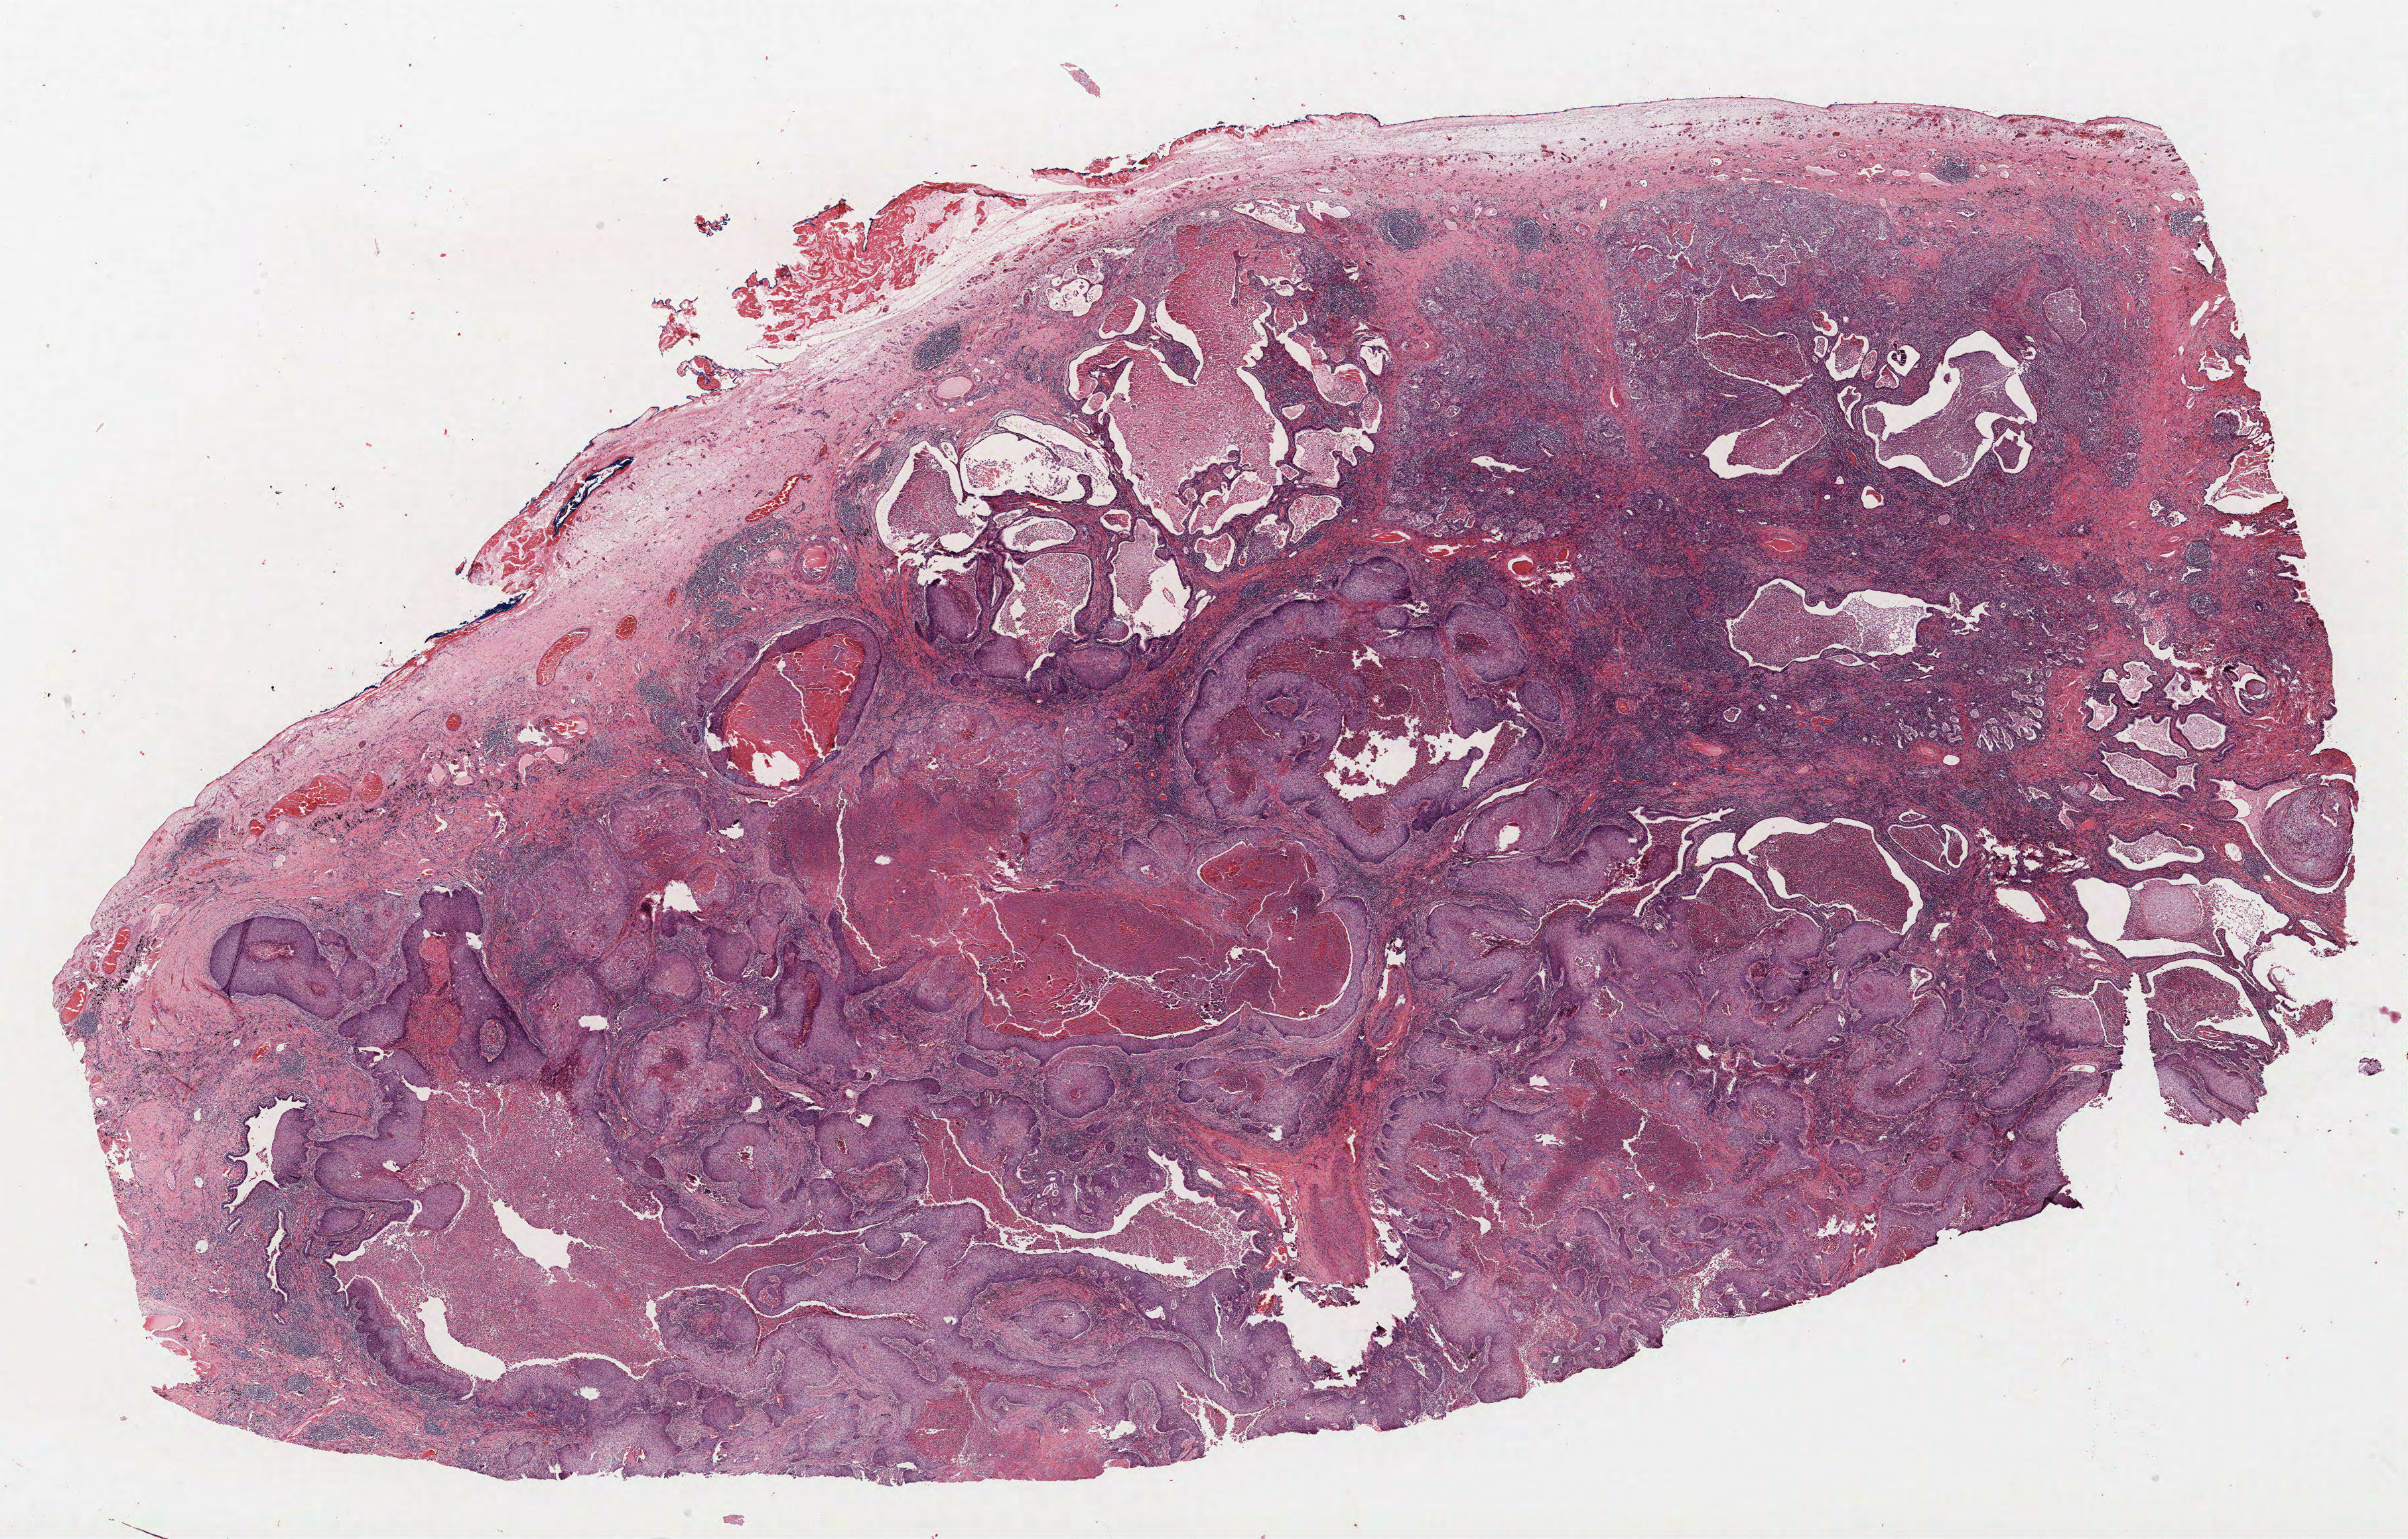
H&E whole-slide image, shown as a low-resolution overview of the whole scanned area (about 29.0 x 18.6 mm, from a 40x scan); FFPE section; lung tissue. Male patient, aged 58 at enrolment. Current smoker at enrolment.
Participant's lung-cancer diagnosis: Squamous cell carcinoma, keratinizing, NOS (ICD-O-3 8071/3). Note: participant had 2 primary lung cancers recorded; fields above describe the first.